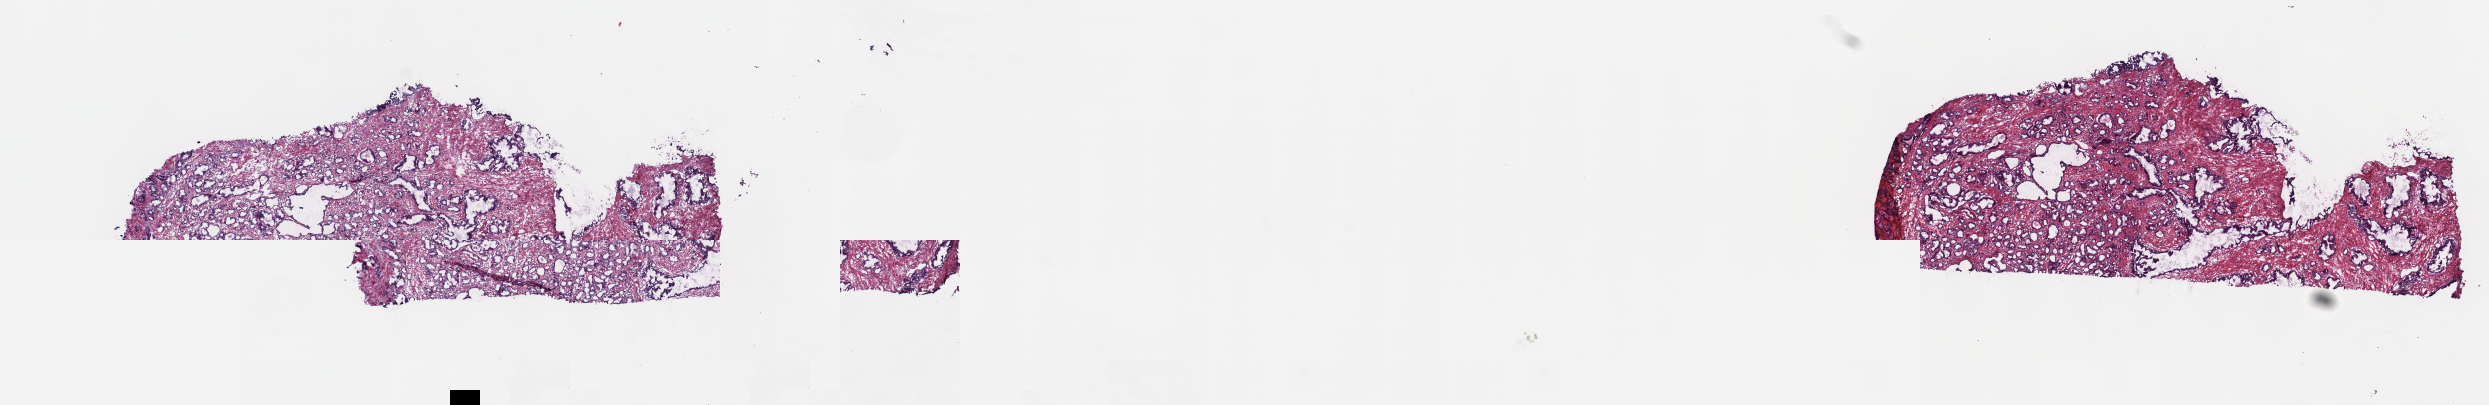
Whole-slide histology image, Hematoxylin and eosin (H&E) stained — low-resolution overview of the scanned area, about 20.1 x 3.3 mm (slide scanned at 40x); frozen section; prostate, primary tumour sample. Male, age 65 years at initial diagnosis. Gleason score: 6 (3+3). Slide review estimates, as recorded: tumour cells 55%, tumour nuclei 70%, normal cells 15%, stromal cells 30%, necrosis 0%. Inflammatory infiltration, as recorded: lymphocyte infiltration 0%, monocyte infiltration 0%, neutrophil infiltration 0%.
- lymph nodes positive (case pathology): 0 of 5 examined
- laterality: right
- diagnosis: Adenocarcinoma, NOS (prostate gland)